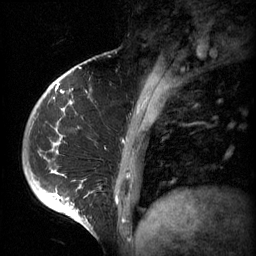
Breast MRI (dynamic contrast-enhanced), one sagittal slice; position 17 of 60 along the scan axis; 3 images stored at this slice position (order not interpretable as contrast timing); 1.5 T; TE 4.2 ms, TR 11 ms; 256 × 256 image matrix, field of view 200 × 200 mm. Female patient, age 51 years.
Outlined on this slice (semi-automatically segmented with operator editing):
- analysis volume of interest (the breast-tissue region the enhancement analysis was run in; not a lesion): bounding box (x1, y1, x2, y2) in pixels: (48, 82, 161, 197)
- tumour enhancement mask (voxels above the 70 % enhancement threshold inside the analysis volume of interest): (48, 82, 159, 197)